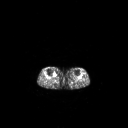
FDG PET of an extremity soft-tissue mass (from a PET/CT study), one axial slice; slice 155 of 267 in the series (ordered by position); 3.27 mm slice thickness; 128 × 128 image matrix, field of view 700 × 700 mm. Patient: female, 65 years. From the clinical record (not read from this slice): histological type: undifferentiated – high grade; grade: high; site of the primary tumour: right thigh.
Outlined on this slice (expert contour drawn on MRI and transferred to this co-registered scan by the dataset authors):
- gross tumour volume (mass): box from (x=53, y=72) to (x=56, y=77) px